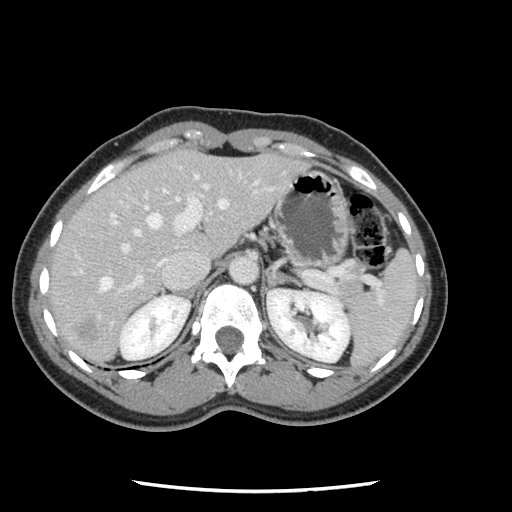
Contrast-enhanced abdominal CT, one axial slice. Soft-tissue window (W 400 / L 40 HU). 2.5 mm slice thickness. 512 × 512 image matrix, field of view 330 × 330 mm. Female patient, age 43 years. From the clinical record (not read from this slice): diagnosis: colorectal cancer liver metastases, imaged before liver resection; multiple liver metastases: yes; largest metastasis: 3.4 cm; chemotherapy before resection: no.
Structures marked on this image (manually delineated by an expert):
- hepatic veins: bounding box (x1, y1, x2, y2) in pixels: (100, 174, 229, 292)
- liver: (49, 152, 304, 364)
- planned liver remnant (the part of the liver to remain after resection): (49, 155, 190, 307)
- portal vein (with intrahepatic branches): (108, 184, 273, 294)
- liver metastasis: (79, 319, 101, 345)